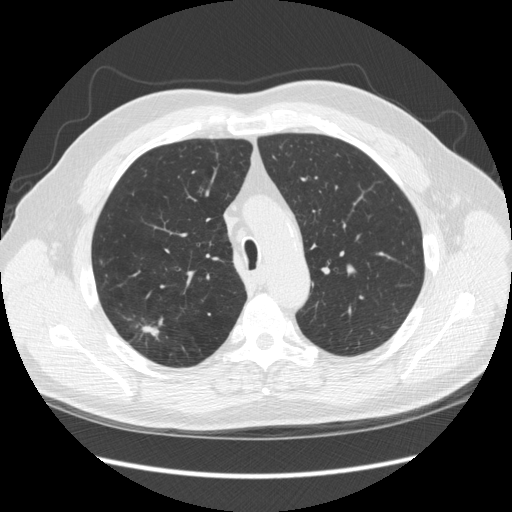
Low-dose screening chest CT, one axial slice. Position 182 of 248 along the scan axis. Reconstruction kernel STANDARD. Lung window (W 1500 / L -600 HU). 2.5 mm slice thickness. 512 × 512 image matrix, field of view 380 × 380 mm.
Structures marked on this image (manually delineated by an expert):
- lesion 1 (tumor, upper lobe of right lung): bounding box <142,326,159,336> (left, top, right, bottom; pixels)